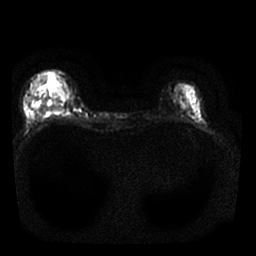
Breast MRI, one axial slice. Position 7 of 25 along the scan axis. Diffusion-weighted series; image 2 of 4 stored at this slice position (different b-values; order by instance number). 1.5 T. 256 × 256 image matrix, field of view 310 × 310 mm. Female patient.
Annotated regions visible in this slice (expert manual segmentation):
- tumour on diffusion-weighted imaging: box from (x=57, y=87) to (x=66, y=97) px